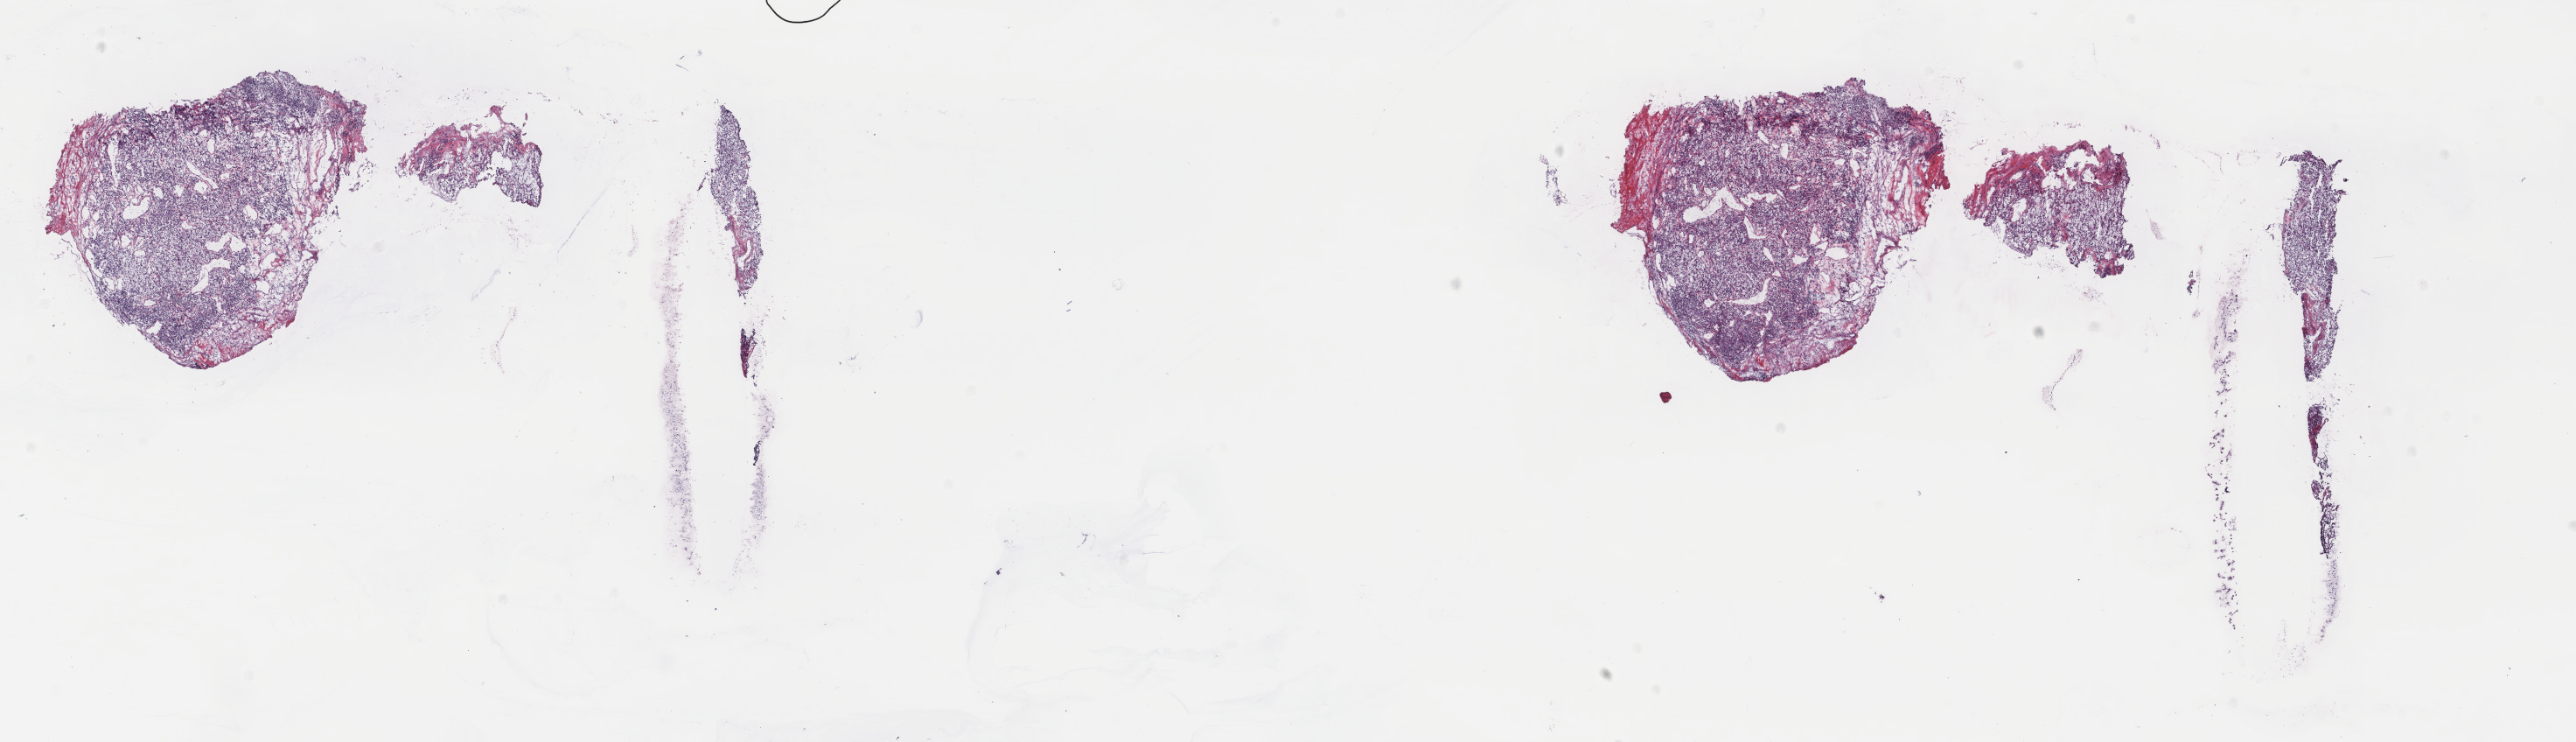
H&E-stained whole-slide image — low-resolution overview of the scanned area, about 23.4 x 6.7 mm, frozen section from the top of the tissue portion, primary tumour sample from the kidney. Patient: male, age at initial diagnosis 61 years. Composition of this section per pathologist review: tumour cells 75%, tumour nuclei 100%.
Pathologic diagnosis: Clear cell adenocarcinoma, NOS.